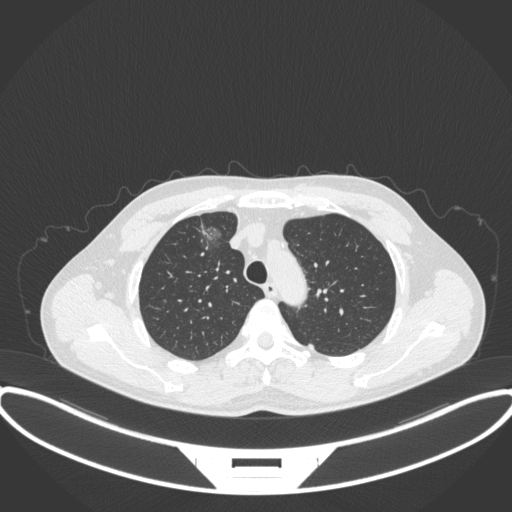
Chest CT, one axial slice; position 282 of 395 along the scan axis; reconstruction kernel B31f; 120 kVp; lung window (W 1500 / L -600 HU); 1 mm slice thickness; 512 × 512 image matrix, field of view 424 × 424 mm. Male patient, age 60 years. From the clinical record (not read from this slice): clinical TNM (as recorded): T1c N0 M0.
Structures marked on this image (rectangle marked by the reading radiologist):
- lung tumour (recorded histology: adenocarcinoma): bounding box [x1, y1, x2, y2] px = [194, 218, 230, 265]